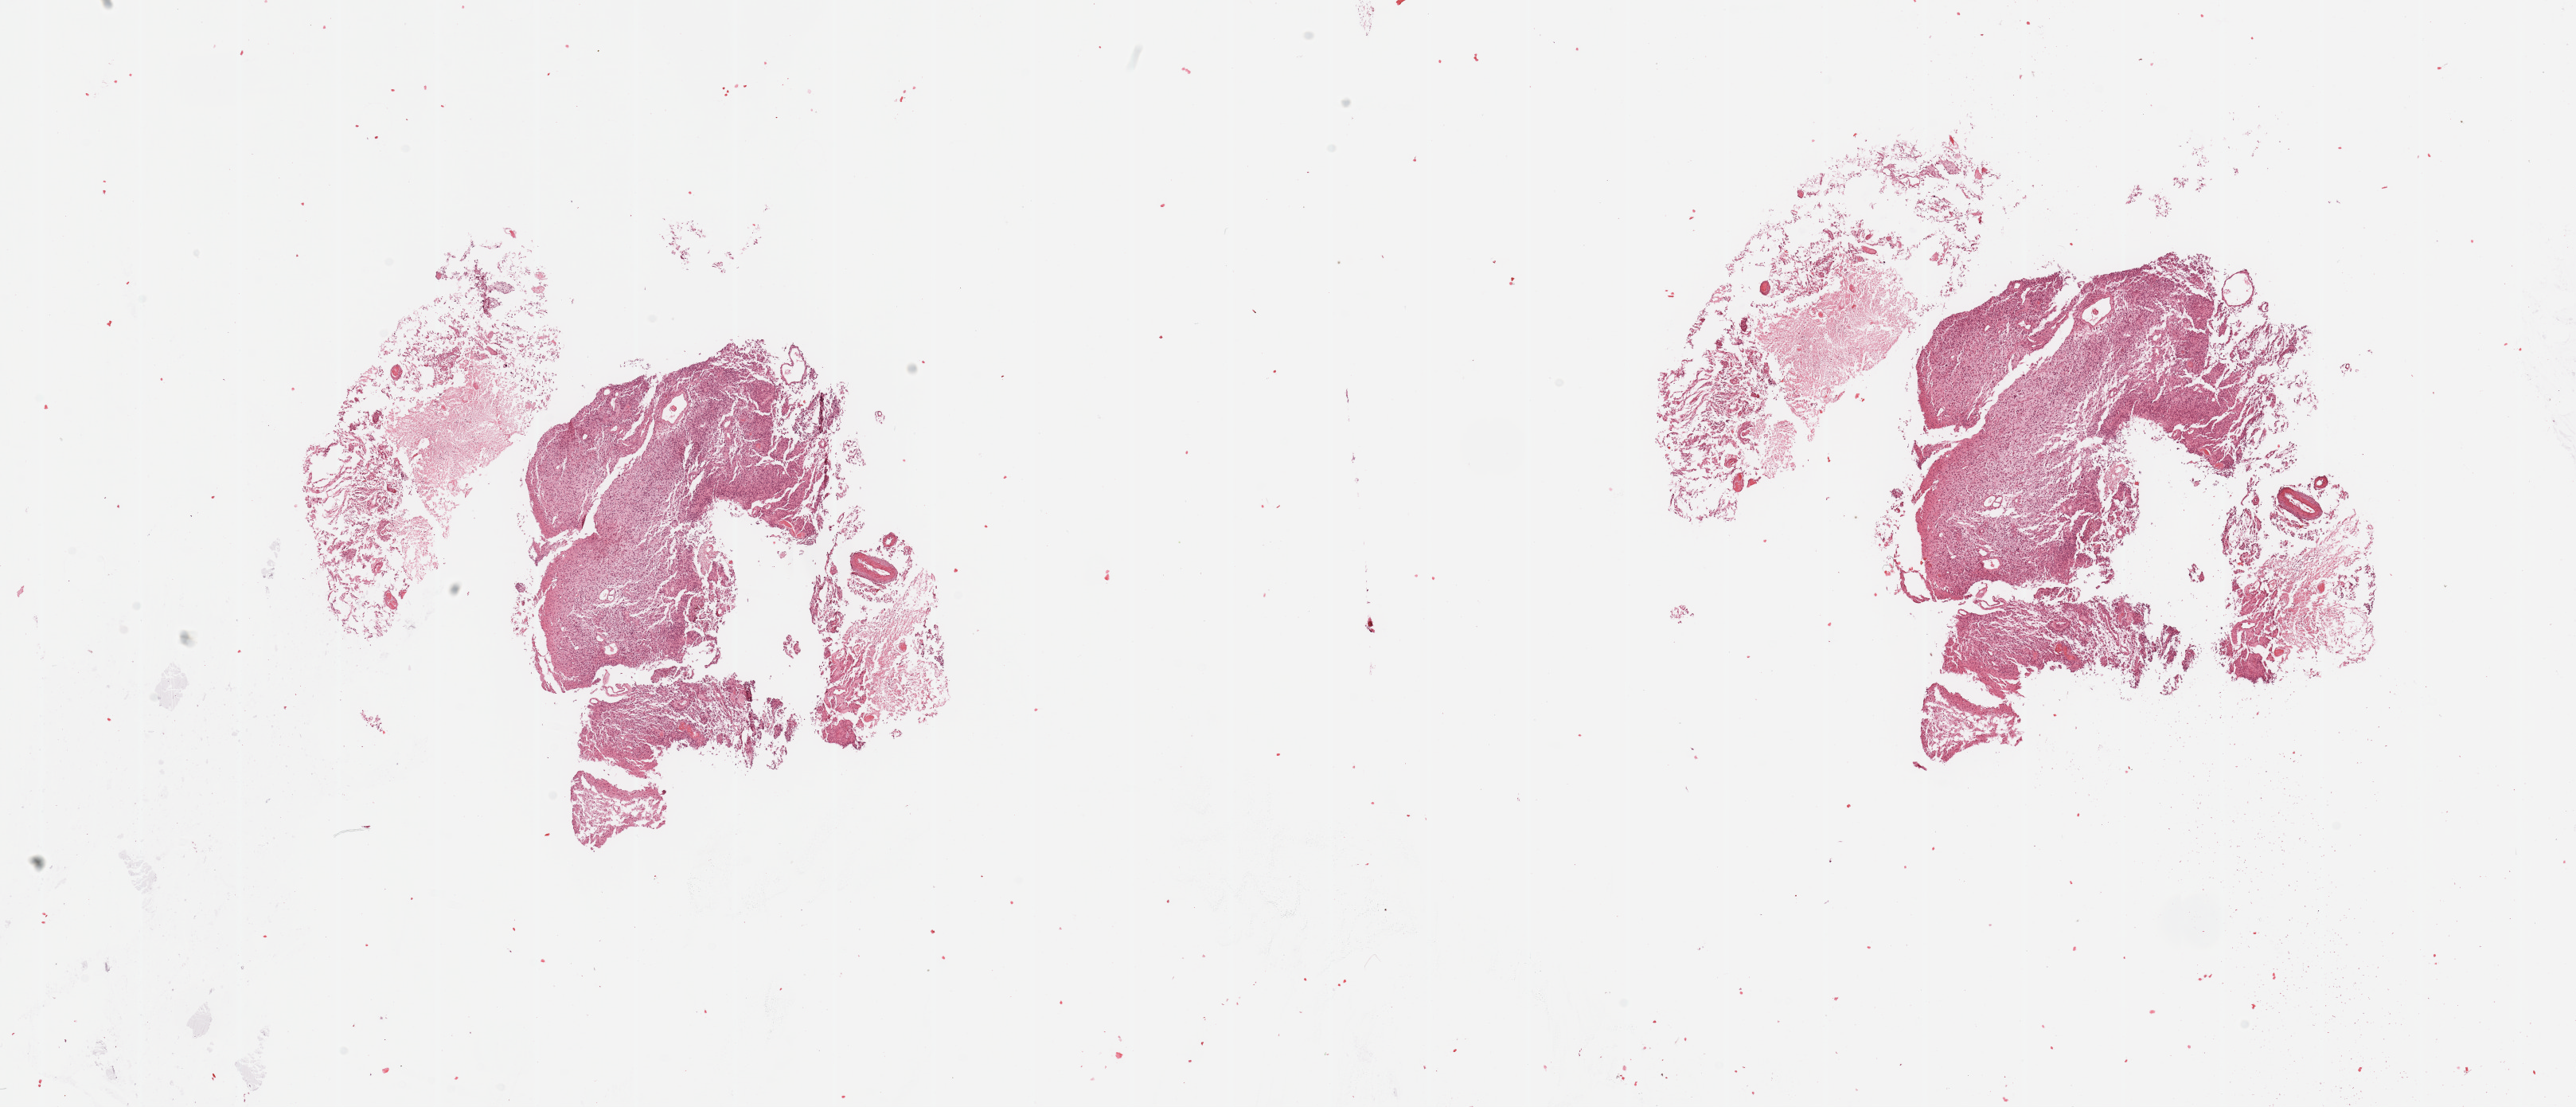
H&E whole-slide image, a low-resolution overview of the entire scanned area, about 25.6 x 11.0 mm (slide scanned at 20x), brain, tumour tissue. Female, 77 y/o.
Histologic diagnosis: Glioblastoma. Primary tumour site (as recorded): temporal lobe.